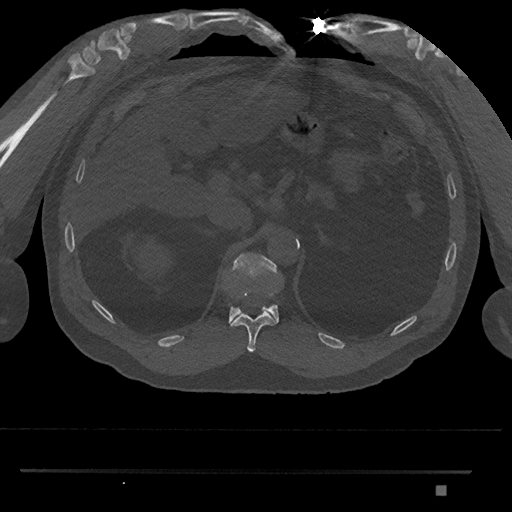
CT including the spine, one axial slice; position 923 of 1134 along the scan axis; reconstruction kernel Br40s/3; 120 kVp; bone window (W 1800 / L 400 HU); 0.5 mm slice thickness; 512 × 512 image matrix. Male patient, age 65 years. Case-level facts recorded for this patient, not image findings: primary cancer: prostate.
Outlined on this slice (semi-automatic segmentation, software-assisted and operator-edited):
- T11 vertebra: bounding box <230,293,277,352> (left, top, right, bottom; pixels)
- T12 vertebra: <228,252,279,323>